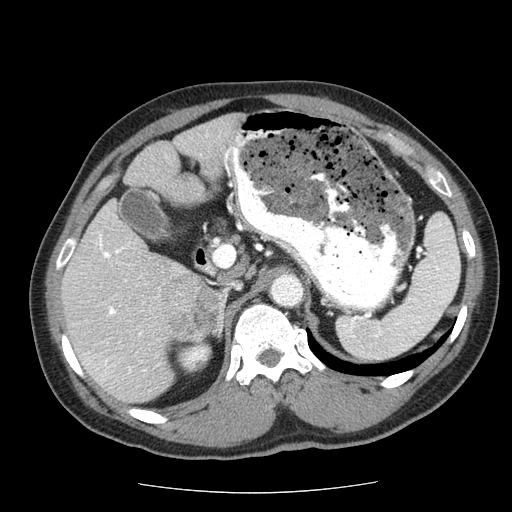
Contrast-enhanced abdominal CT (liver protocol), one axial slice. Reconstruction kernel STANDARD. 120 kVp. Soft-tissue window (W 400 / L 40 HU). 2.5 mm slice thickness. 512 × 512 image matrix, field of view 360 × 360 mm. Case-level facts recorded for this patient, not image findings: diagnosis: hepatocellular carcinoma (patient treated with transarterial chemoembolisation; whether this scan precedes or follows treatment is not stated here); TNM stage (as recorded): Stage-IIIA; Child-Pugh class: A.
Outlined on this slice (semi-automatically segmented with operator editing):
- abdominal aorta: bounding box (x1, y1, x2, y2) in pixels: (272, 276, 301, 304)
- liver parenchyma outside the tumour (the mass and vessels are separate outlines, so this box may not span the whole liver): (60, 114, 240, 402)
- mass: (158, 274, 216, 342)
- liver vessels: (97, 234, 145, 372)